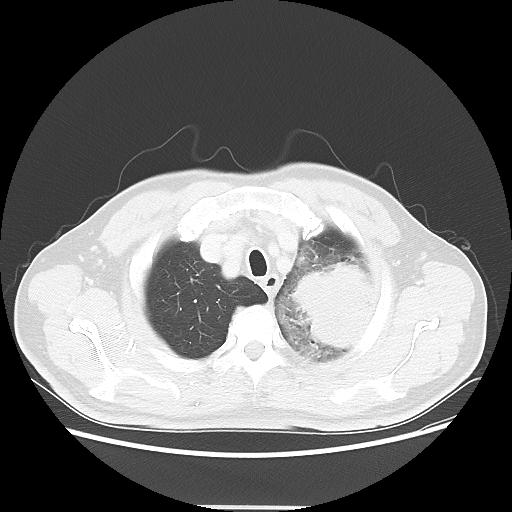
Chest CT, one axial slice; slice 48 of 53 in the series (ordered by position); reconstruction kernel LUNG; 100 kVp; lung window (W 1500 / L -600 HU); 5 mm slice thickness; 512 × 512 image matrix. Patient: male, 60 years. From the clinical record (not read from this slice): clinical TNM (as recorded): T4 N1 M1a.
Structures marked on this image (bounding box drawn by a radiologist):
- lung tumour (recorded histology: large cell carcinoma): bounding box [x1, y1, x2, y2] px = [289, 259, 384, 351]